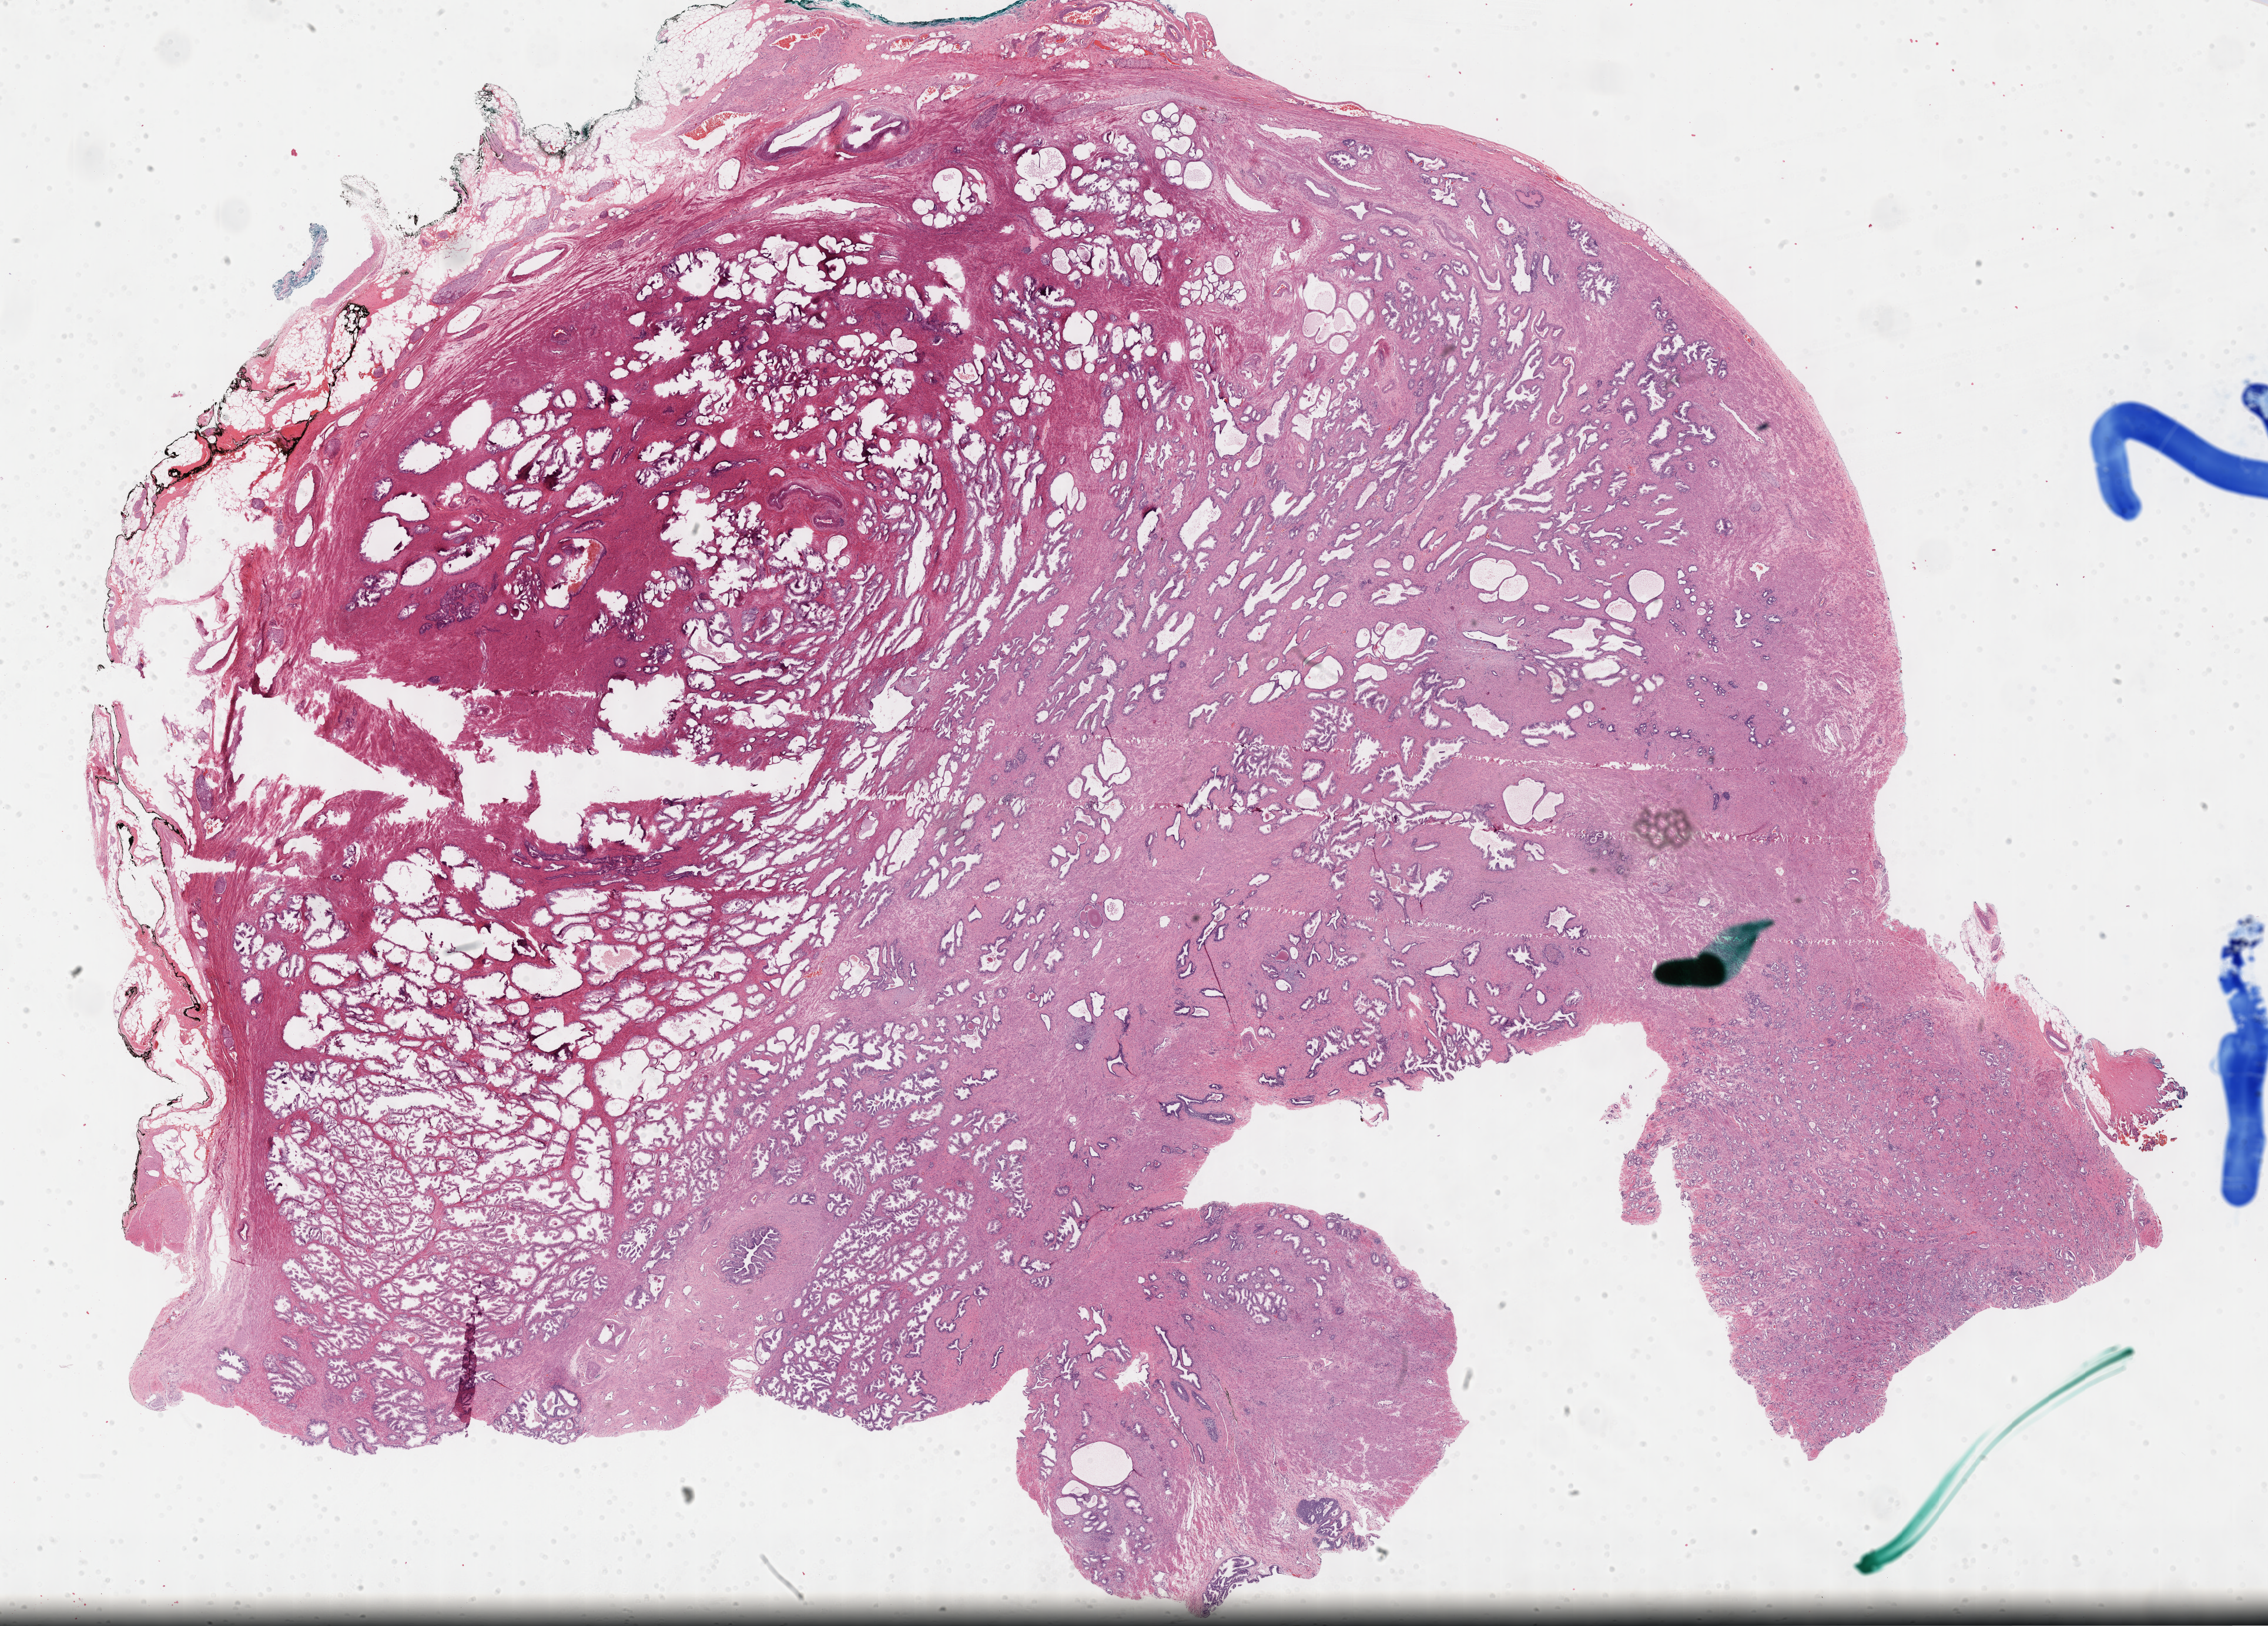
Digitized Hematoxylin and eosin (H&E) stained tissue section (whole slide) — low-resolution overview of the scanned area, about 31.2 x 22.4 mm (acquisition: 40x scan), formalin-fixed paraffin-embedded (FFPE) diagnostic section, sample: primary tumour, prostate. Patient: male, age at initial diagnosis 51 years. Gleason score: 7 (3+4).
Lymph nodes positive (case pathology): 0 of 18 examined. Diagnosis: Adenocarcinoma, NOS (prostate gland).